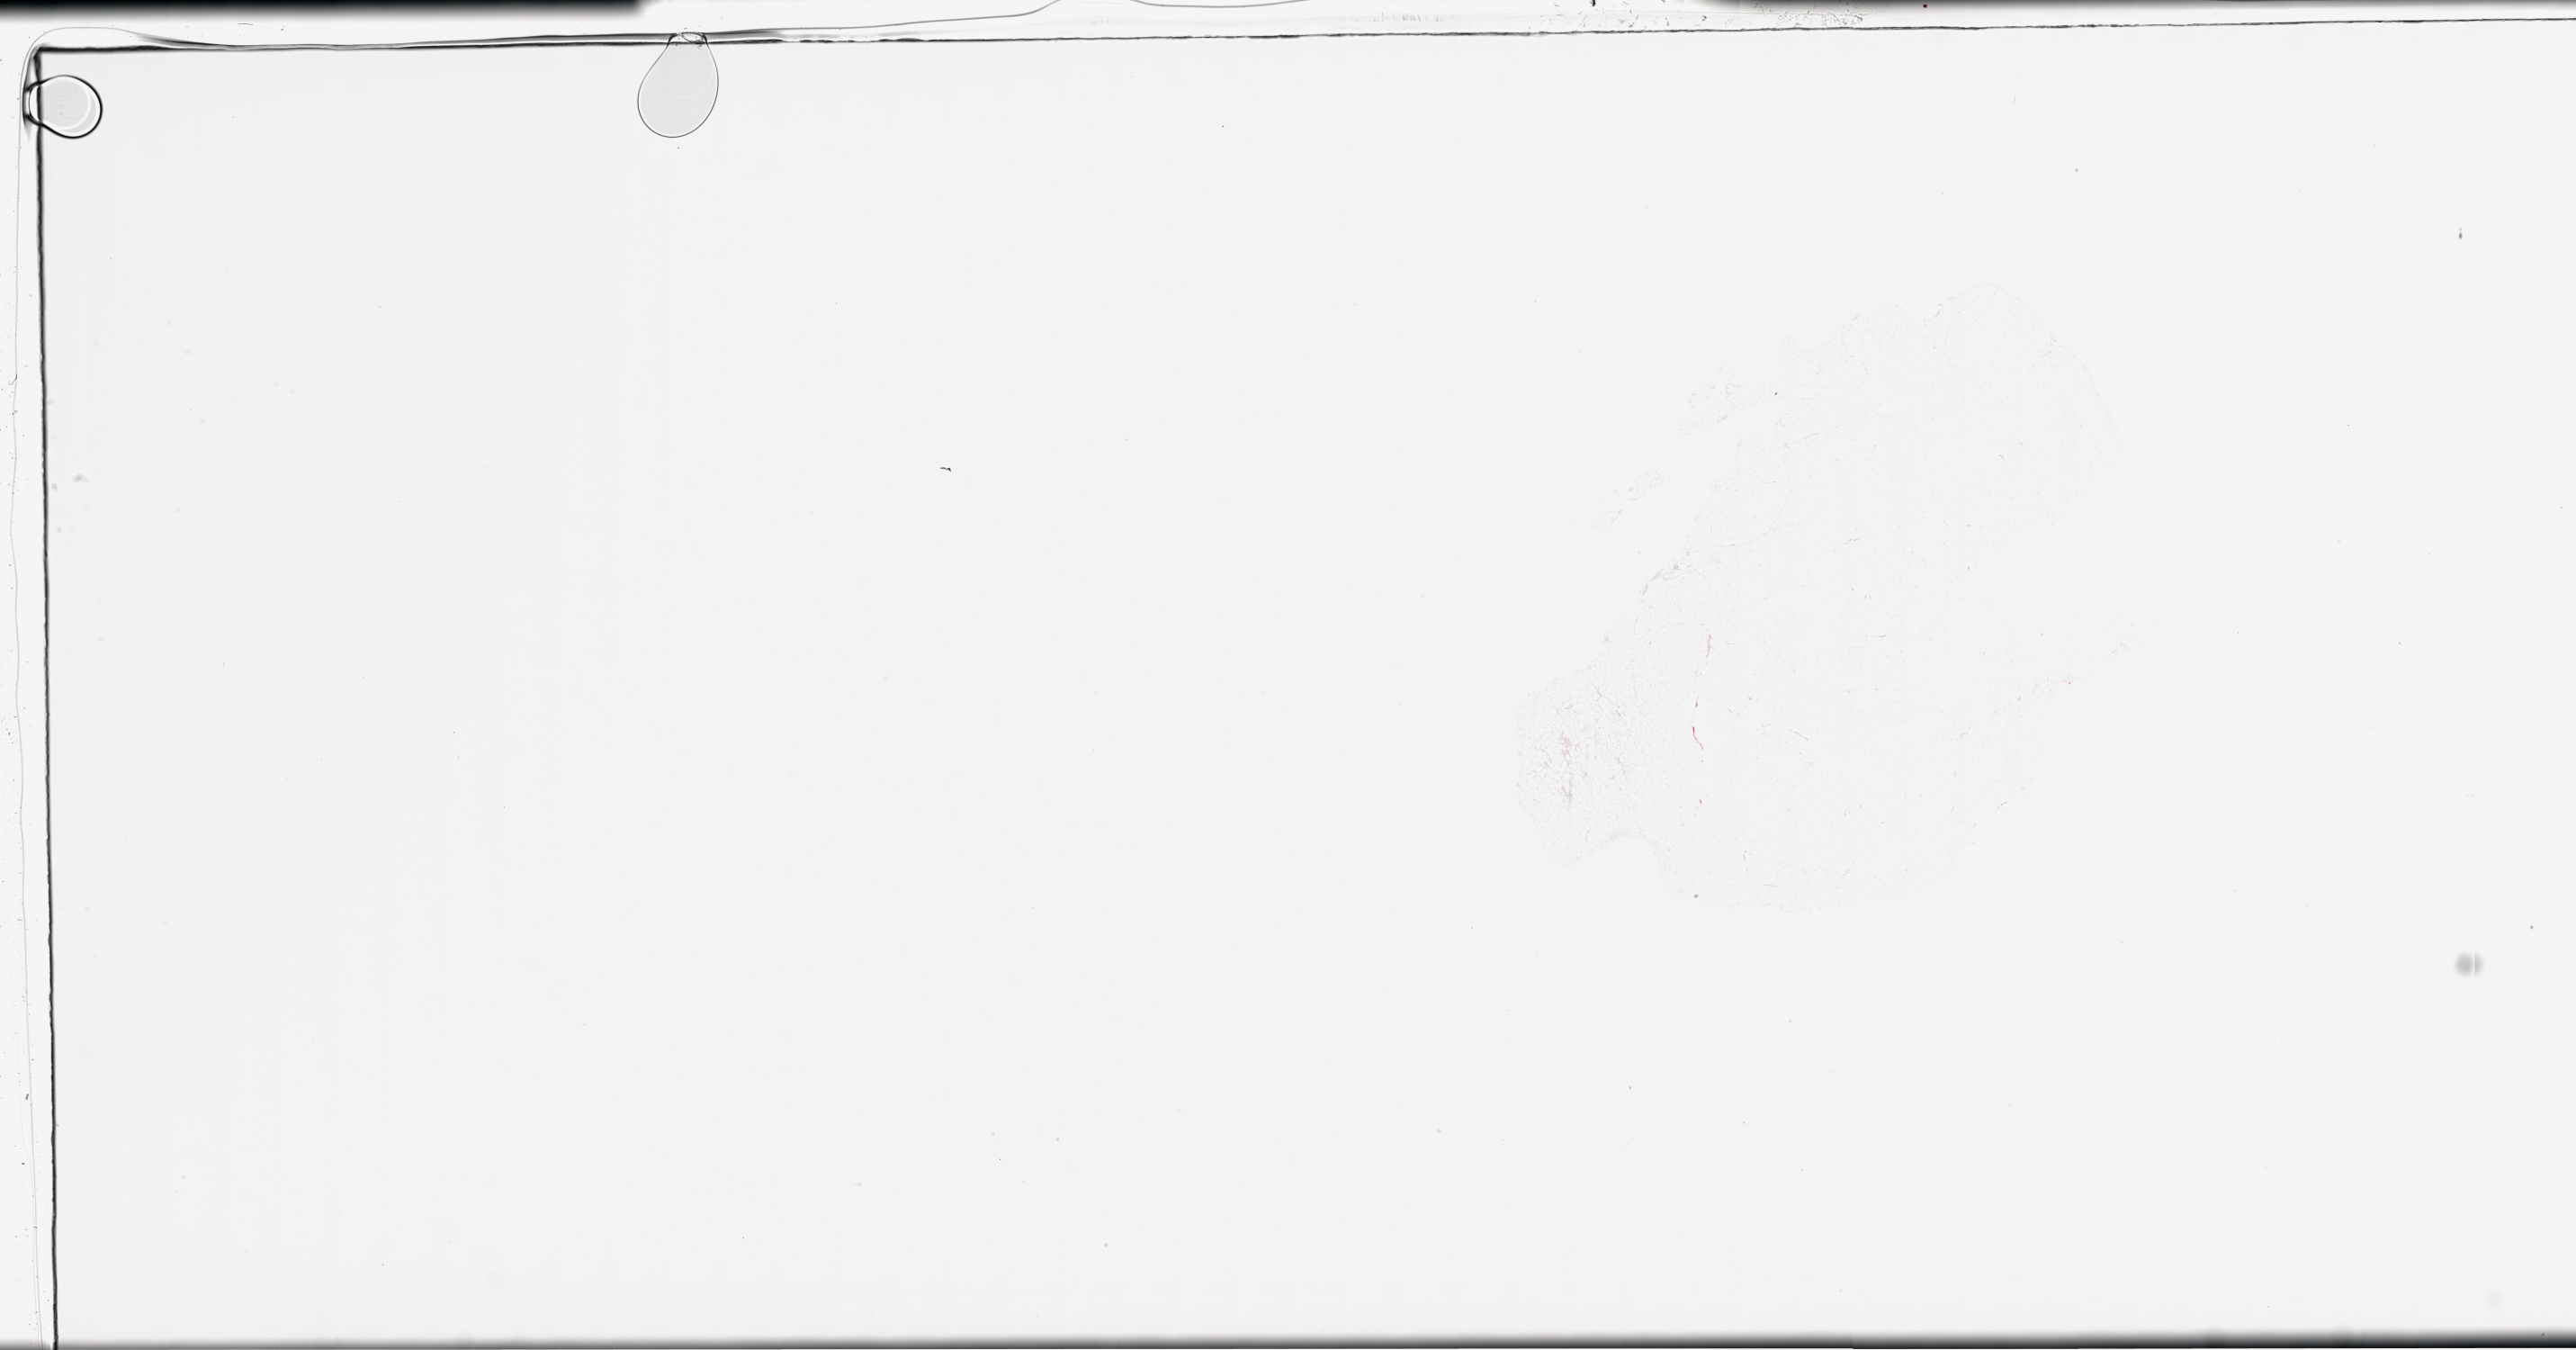
Hematoxylin and eosin (H&E) stained whole-slide image — a low-resolution overview of the entire scanned area, about 46.1 x 24.2 mm (from a 20x scan). Normal (non-tumour) tissue sample. Female, 58 y/o.
This section: normal (non-tumour) tissue from the same patient. Patient diagnosis (cohort enrolment): sarcoma (site not recorded at cohort level).